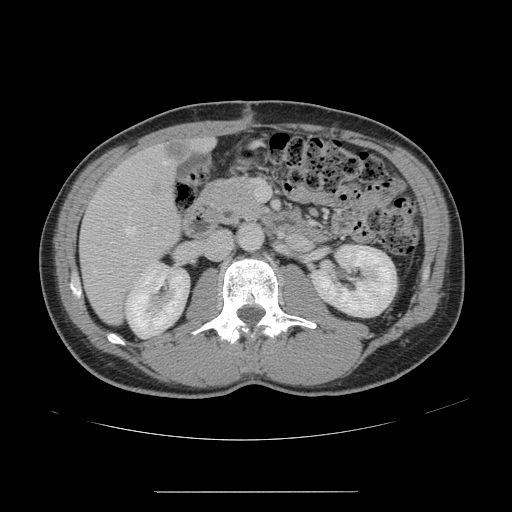
Contrast-enhanced abdominal CT, one axial slice; position 63 of 178 along the scan axis; intravenous contrast given; soft-tissue window (W 400 / L 40 HU); 2.5 mm slice thickness; 512 × 512 image matrix, field of view 401 × 401 mm. Male patient, age 53 years. Case-level facts recorded for this patient, not image findings: diagnosis: colorectal cancer liver metastases, imaged before liver resection; multiple liver metastases: yes; largest metastasis: 2.4 cm; disease in both lobes: no.
Annotated regions visible in this slice (expert manual segmentation):
- hepatic veins: bounding box [x1, y1, x2, y2] px = [94, 160, 169, 273]
- liver: [81, 140, 208, 322]
- planned liver remnant (the part of the liver to remain after resection): [200, 142, 209, 148]
- portal vein (with intrahepatic branches): [255, 181, 267, 201]
- liver metastasis: [165, 140, 194, 161]